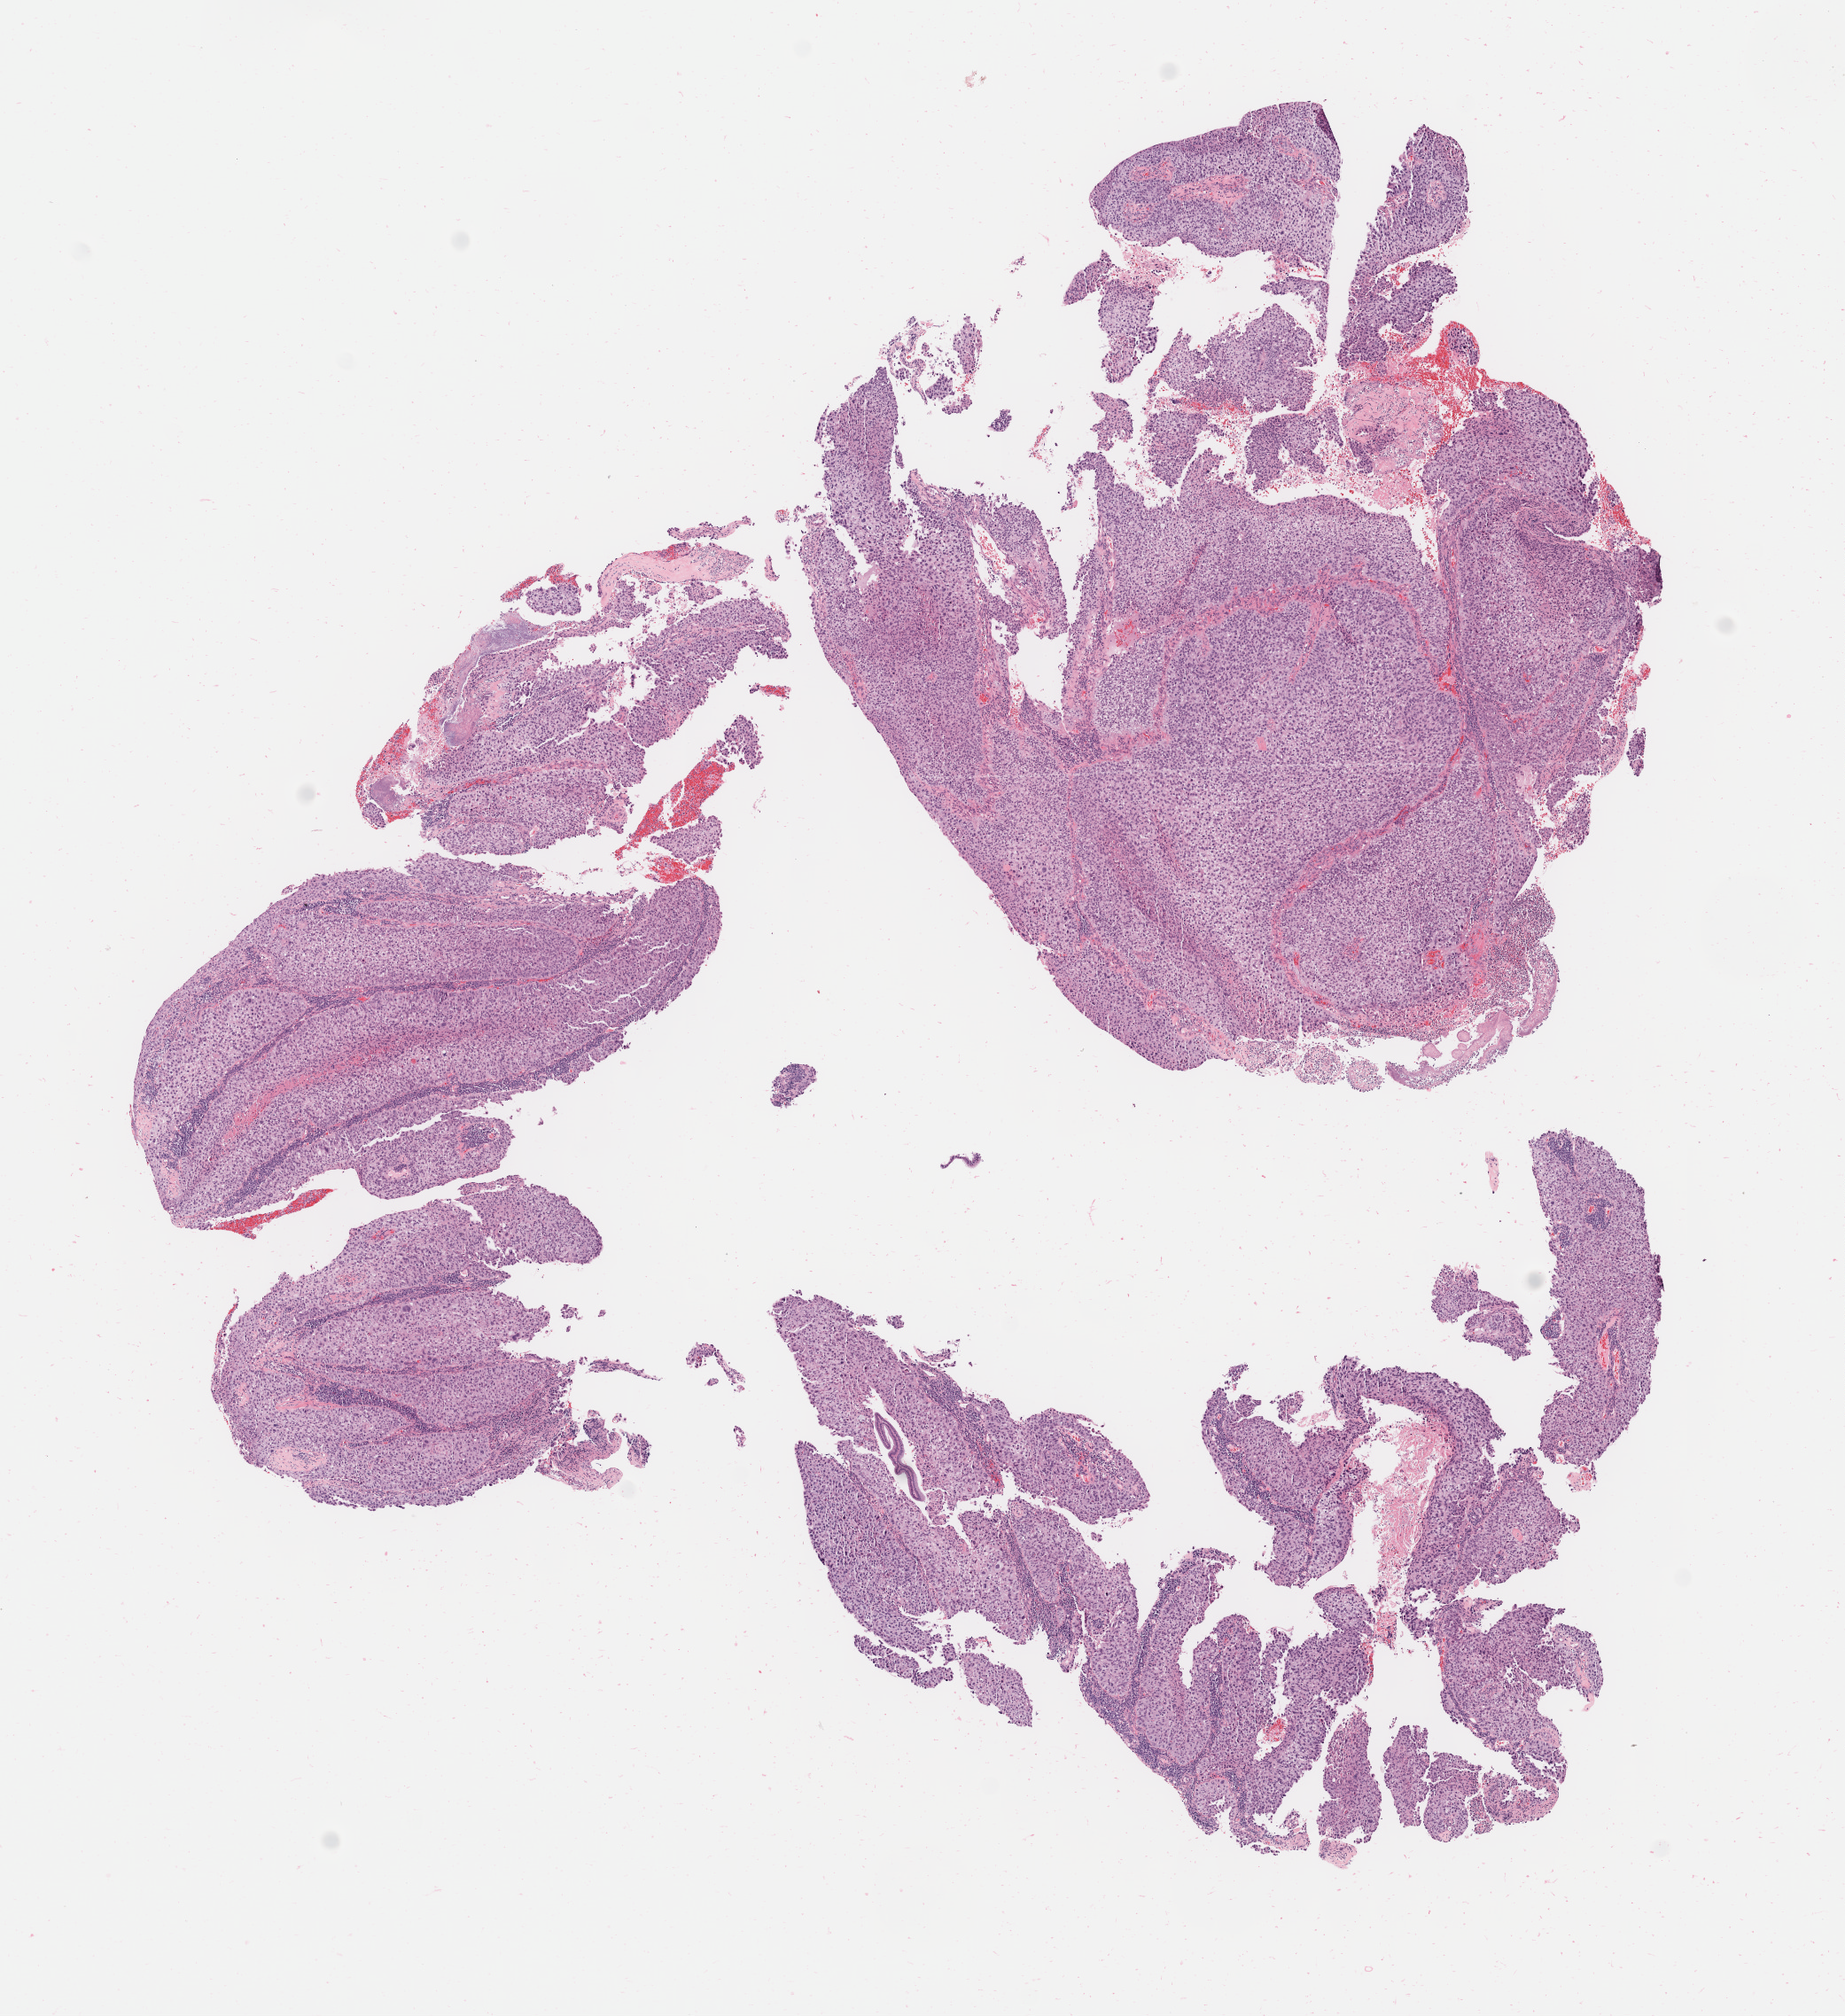
Hematoxylin and eosin (H&E) whole-slide image, shown as a low-resolution overview of the whole scanned area (about 8.3 x 9.1 mm), specimen: tumor tissue, anatomic site: cervix. Patient female; aged 50.
Histologic diagnosis: Squamous cell carcinoma, large cell, nonkeratinizing, NOS.